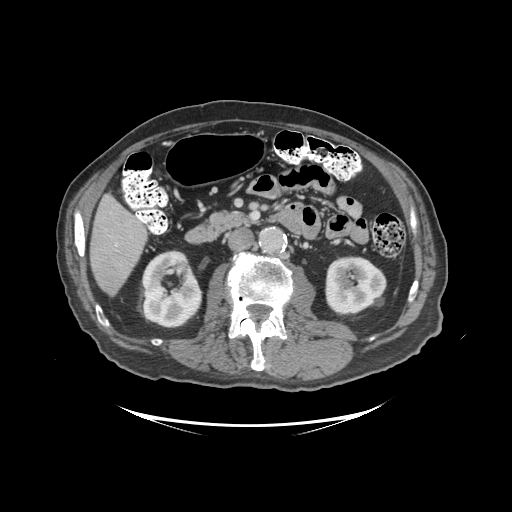
Contrast-enhanced abdominal CT (liver protocol), one axial slice. Position 36 of 99 along the scan axis. Soft-tissue window (W 400 / L 40 HU). 2.5 mm slice thickness. 512 × 512 image matrix. Case-level facts recorded for this patient, not image findings: diagnosis: hepatocellular carcinoma (patient treated with transarterial chemoembolisation; whether this scan precedes or follows treatment is not stated here); TNM stage (as recorded): Stage-I; Child-Pugh class: A.
Structures marked on this image (semi-automatically segmented with operator editing):
- liver parenchyma outside the tumour (the mass and vessels are separate outlines, so this box may not span the whole liver): bounding box (x1, y1, x2, y2) in pixels: (90, 194, 146, 296)